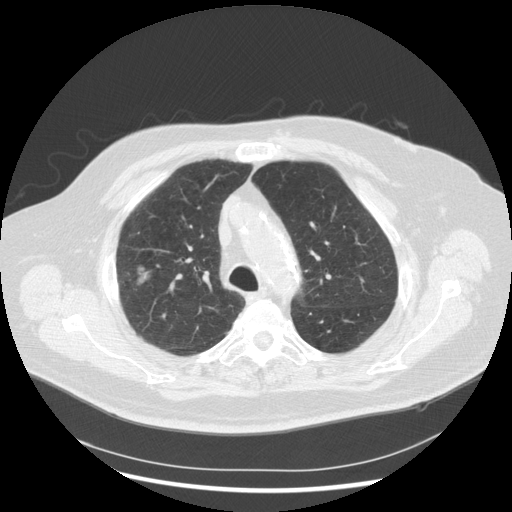
Chest CT (low-dose screening protocol), one axial image. Third screening round (two years after baseline). Lung window (W 1500 / L -600 HU). Slice 207 of 263 in the series. 512 × 512 image matrix, field of view 400 × 400 mm. Male participant, aged 72 years at enrolment. Former smoker at enrolment.
Lesion marked by an expert reader, bounding box (x1, y1, x2, y2) in pixels: (112, 252, 166, 303). The exam's reader record, not a measurement of the box and not confirmed to be the same lesion: non-calcified nodule or mass ≥4 mm, right upper lobe, 31 × 31 mm, poorly defined margins, soft tissue attenuation, pre-existing on the prior screen: no. Official screen result: positive, other. Participant outcome: lung cancer diagnosed 70 days after this screen — squamous cell carcinoma, NOS, right upper lobe, poorly differentiated (G3), stage IIIA (AJCC 6th edition), 19 mm at pathology.